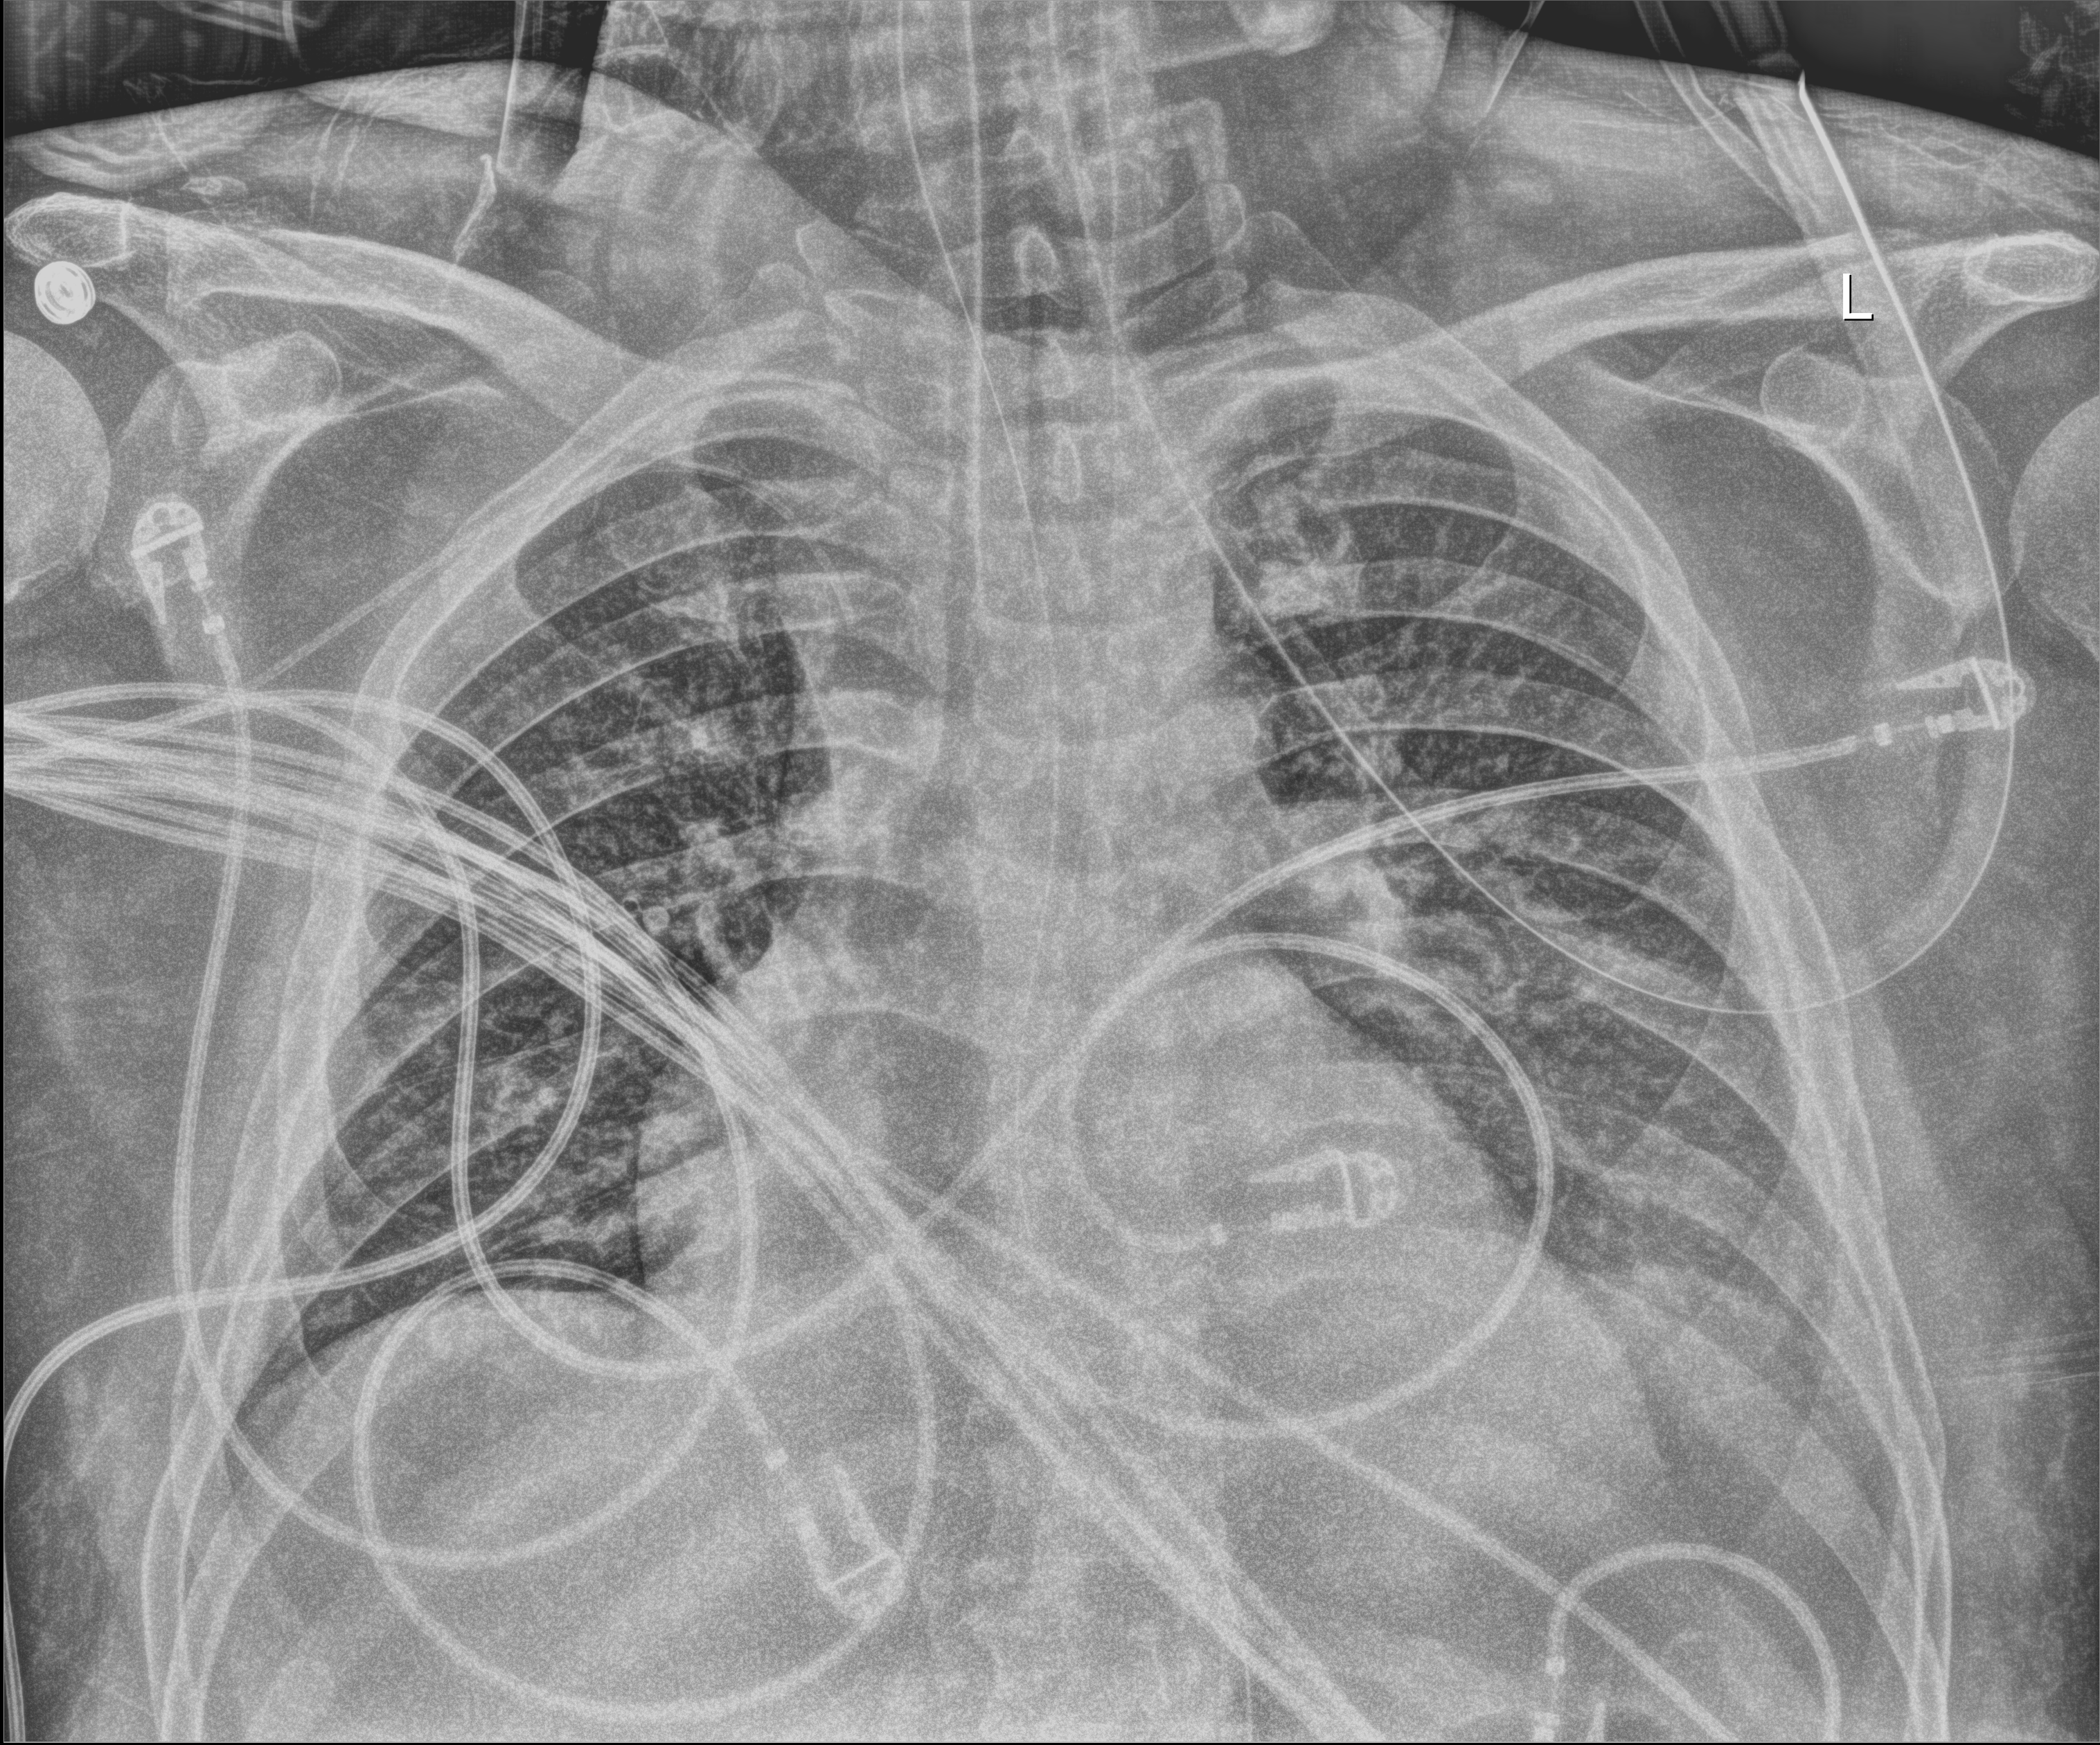
Bedside chest radiograph (digital radiography); anteroposterior (AP) projection. Male patient hospitalised with COVID-19, age 18–59 years.
From the hospital-stay record, not from the radiograph (when in the stay this image was taken is not recorded):
- mechanically ventilated during this hospital stay: yes